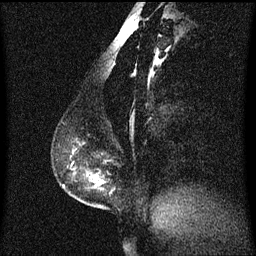
Breast MRI (dynamic contrast-enhanced), one sagittal slice. Dynamic contrast-enhanced series, image 2 of 3 at this slice position (ordered by acquisition). 1.5 T. TE 4.2 ms, TR 8.4 ms. 2 mm slice thickness. 256 × 256 image matrix, field of view 200 × 200 mm. Patient: female, 40 years. From the clinical record (not read from this slice): setting: breast cancer imaged before/during neoadjuvant chemotherapy; receptor status: triple-negative.
Outlined on this slice (semi-automatic segmentation, software-assisted and operator-edited):
- analysis volume of interest (the breast-tissue region the enhancement analysis was run in; not a lesion): bounding box [x1, y1, x2, y2] px = [60, 150, 113, 209]
- tumour enhancement mask (voxels above the 70 % enhancement threshold inside the analysis volume of interest): [100, 182, 103, 185]